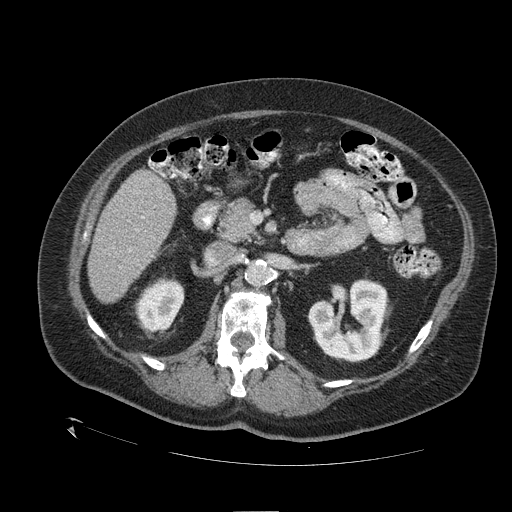
Contrast-enhanced abdominal CT (liver protocol), one axial slice. Slice 52 of 109 in the series (ordered by position). 120 kVp. One of 2 acquisitions stored at this slice position. Soft-tissue window (W 400 / L 40 HU). 2.5 mm slice thickness. 512 × 512 image matrix, field of view 460 × 460 mm. From the clinical record (not read from this slice): diagnosis: hepatocellular carcinoma (patient treated with transarterial chemoembolisation; whether this scan precedes or follows treatment is not stated here); TNM stage (as recorded): Stage-I; Child-Pugh class: A; tumour differentiation: no biopsy; tumour size: 4.6 cm.
Annotated regions visible in this slice (semi-automatically segmented with operator editing):
- liver parenchyma outside the tumour (the mass and vessels are separate outlines, so this box may not span the whole liver): bounding box [x1, y1, x2, y2] px = [88, 170, 176, 302]
- liver vessels: [129, 216, 144, 251]